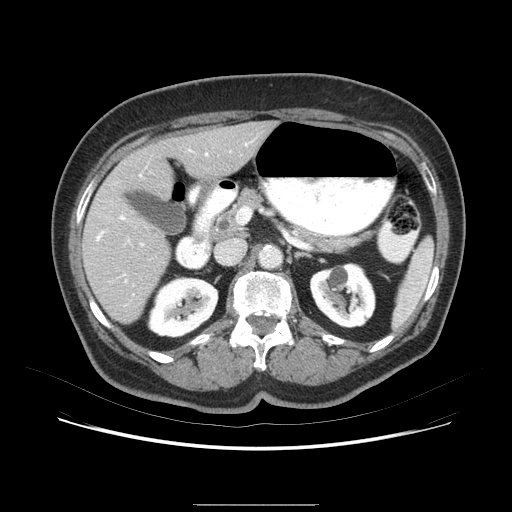
Contrast-enhanced abdominal CT (liver protocol), one axial slice; slice 37 of 79 in the series (ordered by position); 120 kVp; soft-tissue window (W 400 / L 40 HU); 2.5 mm slice thickness; 512 × 512 image matrix, field of view 380 × 380 mm. From the clinical record (not read from this slice): diagnosis: hepatocellular carcinoma (patient treated with transarterial chemoembolisation; whether this scan precedes or follows treatment is not stated here); TNM stage (as recorded): Stage-I; Child-Pugh class: A; tumour differentiation: poorly differentiated; tumour nodularity: uninodular.
Structures marked on this image (semi-automatic segmentation, software-assisted and operator-edited):
- liver parenchyma outside the tumour (the mass and vessels are separate outlines, so this box may not span the whole liver): bounding box [x1, y1, x2, y2] px = [82, 120, 282, 334]
- mass: [117, 201, 162, 243]
- liver vessels: [109, 156, 236, 279]